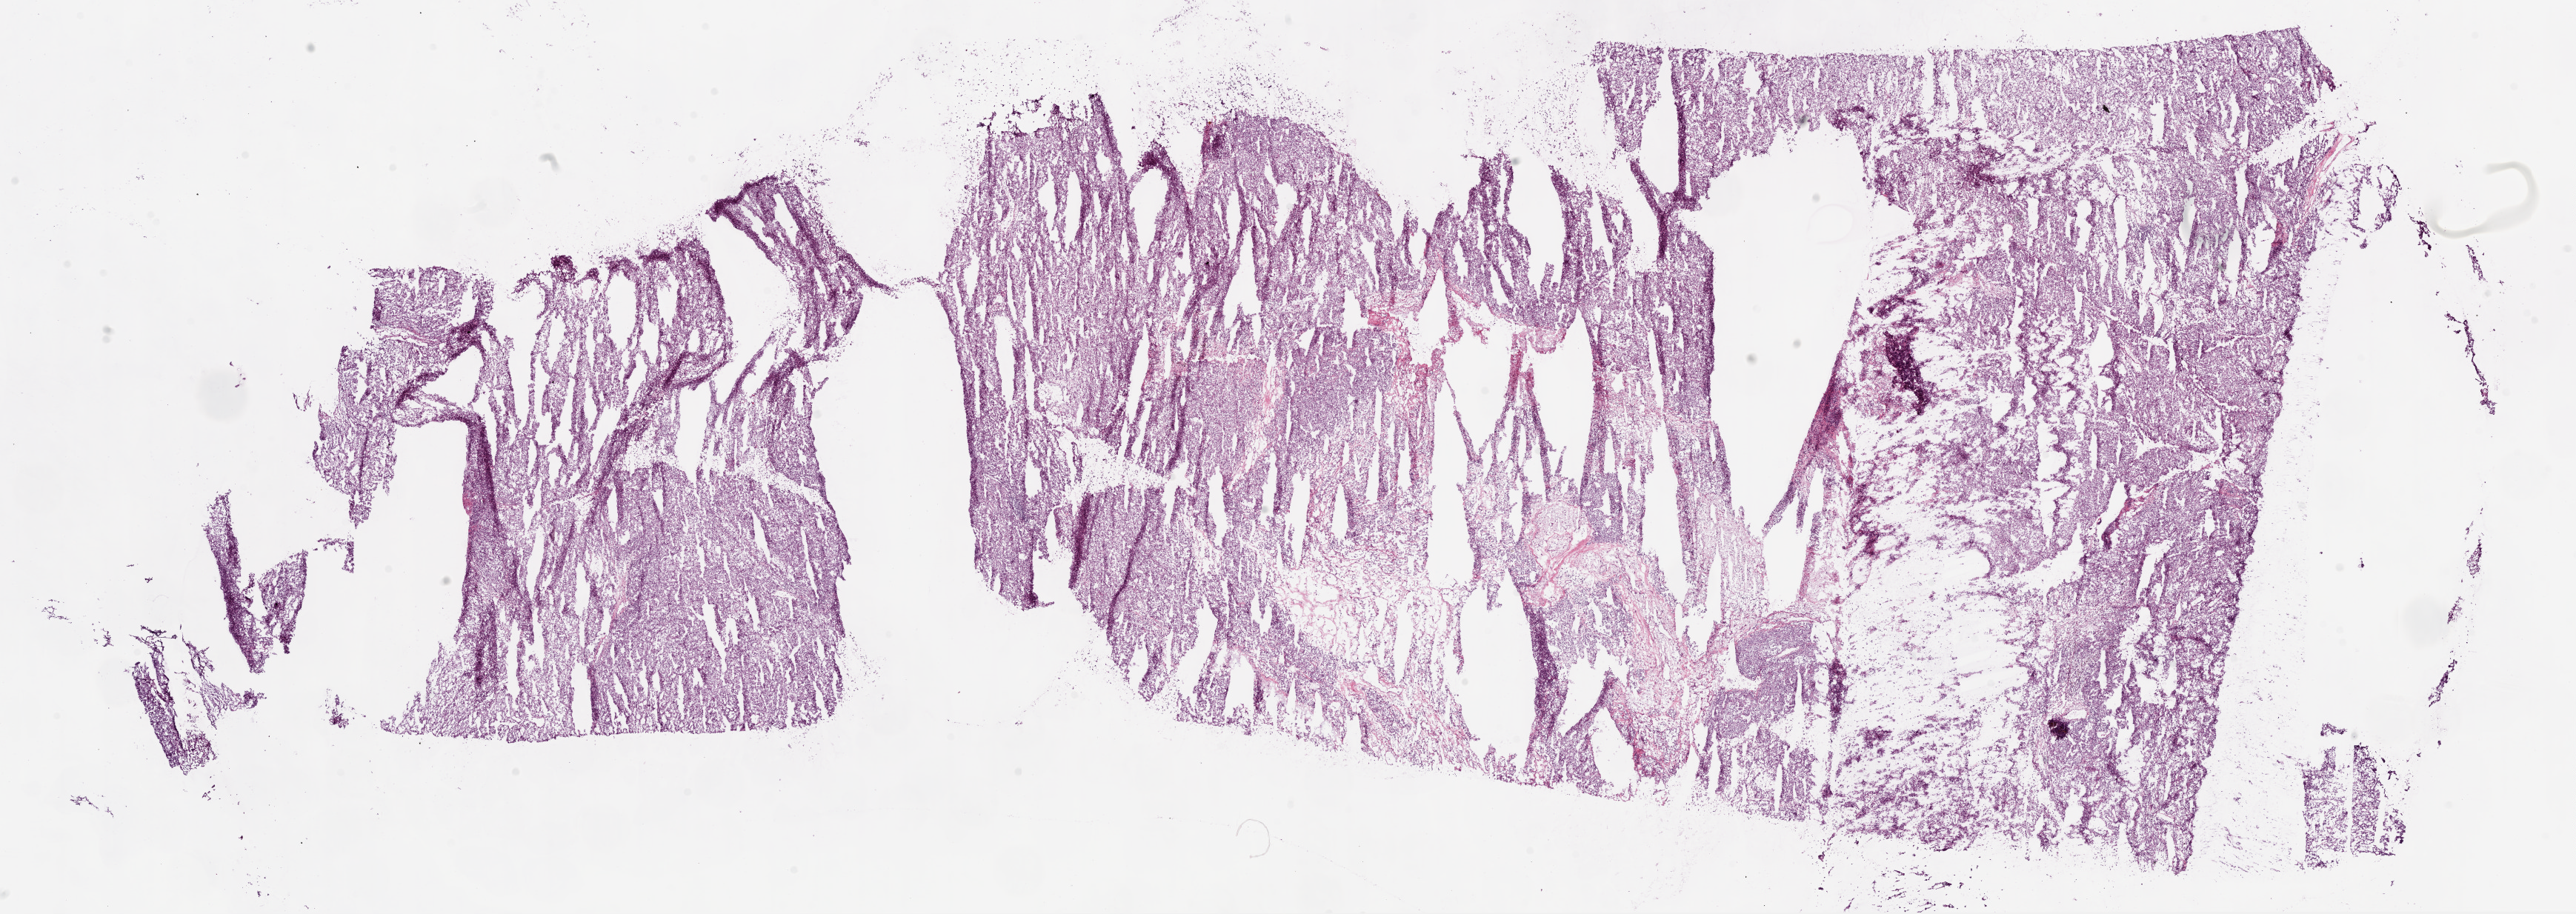
Digitized Hematoxylin and eosin (H&E) stained tissue section (whole slide), low-resolution overview of the scanned area, about 28.0 x 10.0 mm (slide scanned at 20x), frozen section, sample: primary tumour, kidney. Male, age 70 years at initial diagnosis. Histologic grade: G3 (poorly differentiated). Composition of this section per pathologist review: tumour cells 88%, tumour nuclei 85%, normal cells 0%, stromal cells 12%, necrosis 0%.
Laterality: right. Pathologic diagnosis: Clear cell adenocarcinoma, NOS. TNM: T2a NX M0. AJCC pathologic stage: II (7th edition).